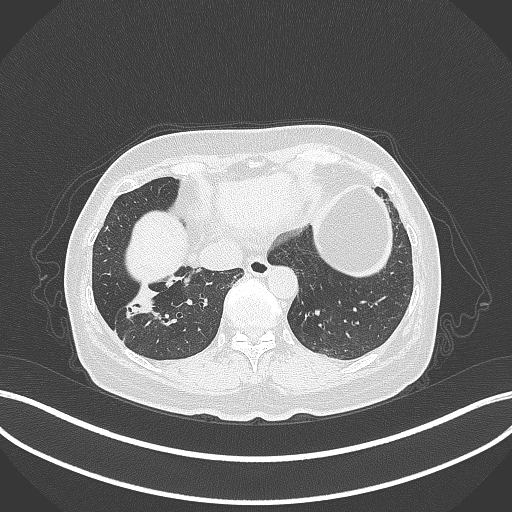
Chest CT, one axial slice. Position 101 of 429 along the scan axis. Reconstruction kernel B70f. 120 kVp. Lung window (W 1500 / L -600 HU). 1 mm slice thickness. 512 × 512 image matrix. Patient: female, 67 years. From the clinical record (not read from this slice): clinical TNM (as recorded): T1c N1 M0; histopathological grade: G2-3.
Structures marked on this image (bounding box drawn by a radiologist):
- lung tumour (recorded histology: adenocarcinoma): bounding box <118,288,163,327> (left, top, right, bottom; pixels)